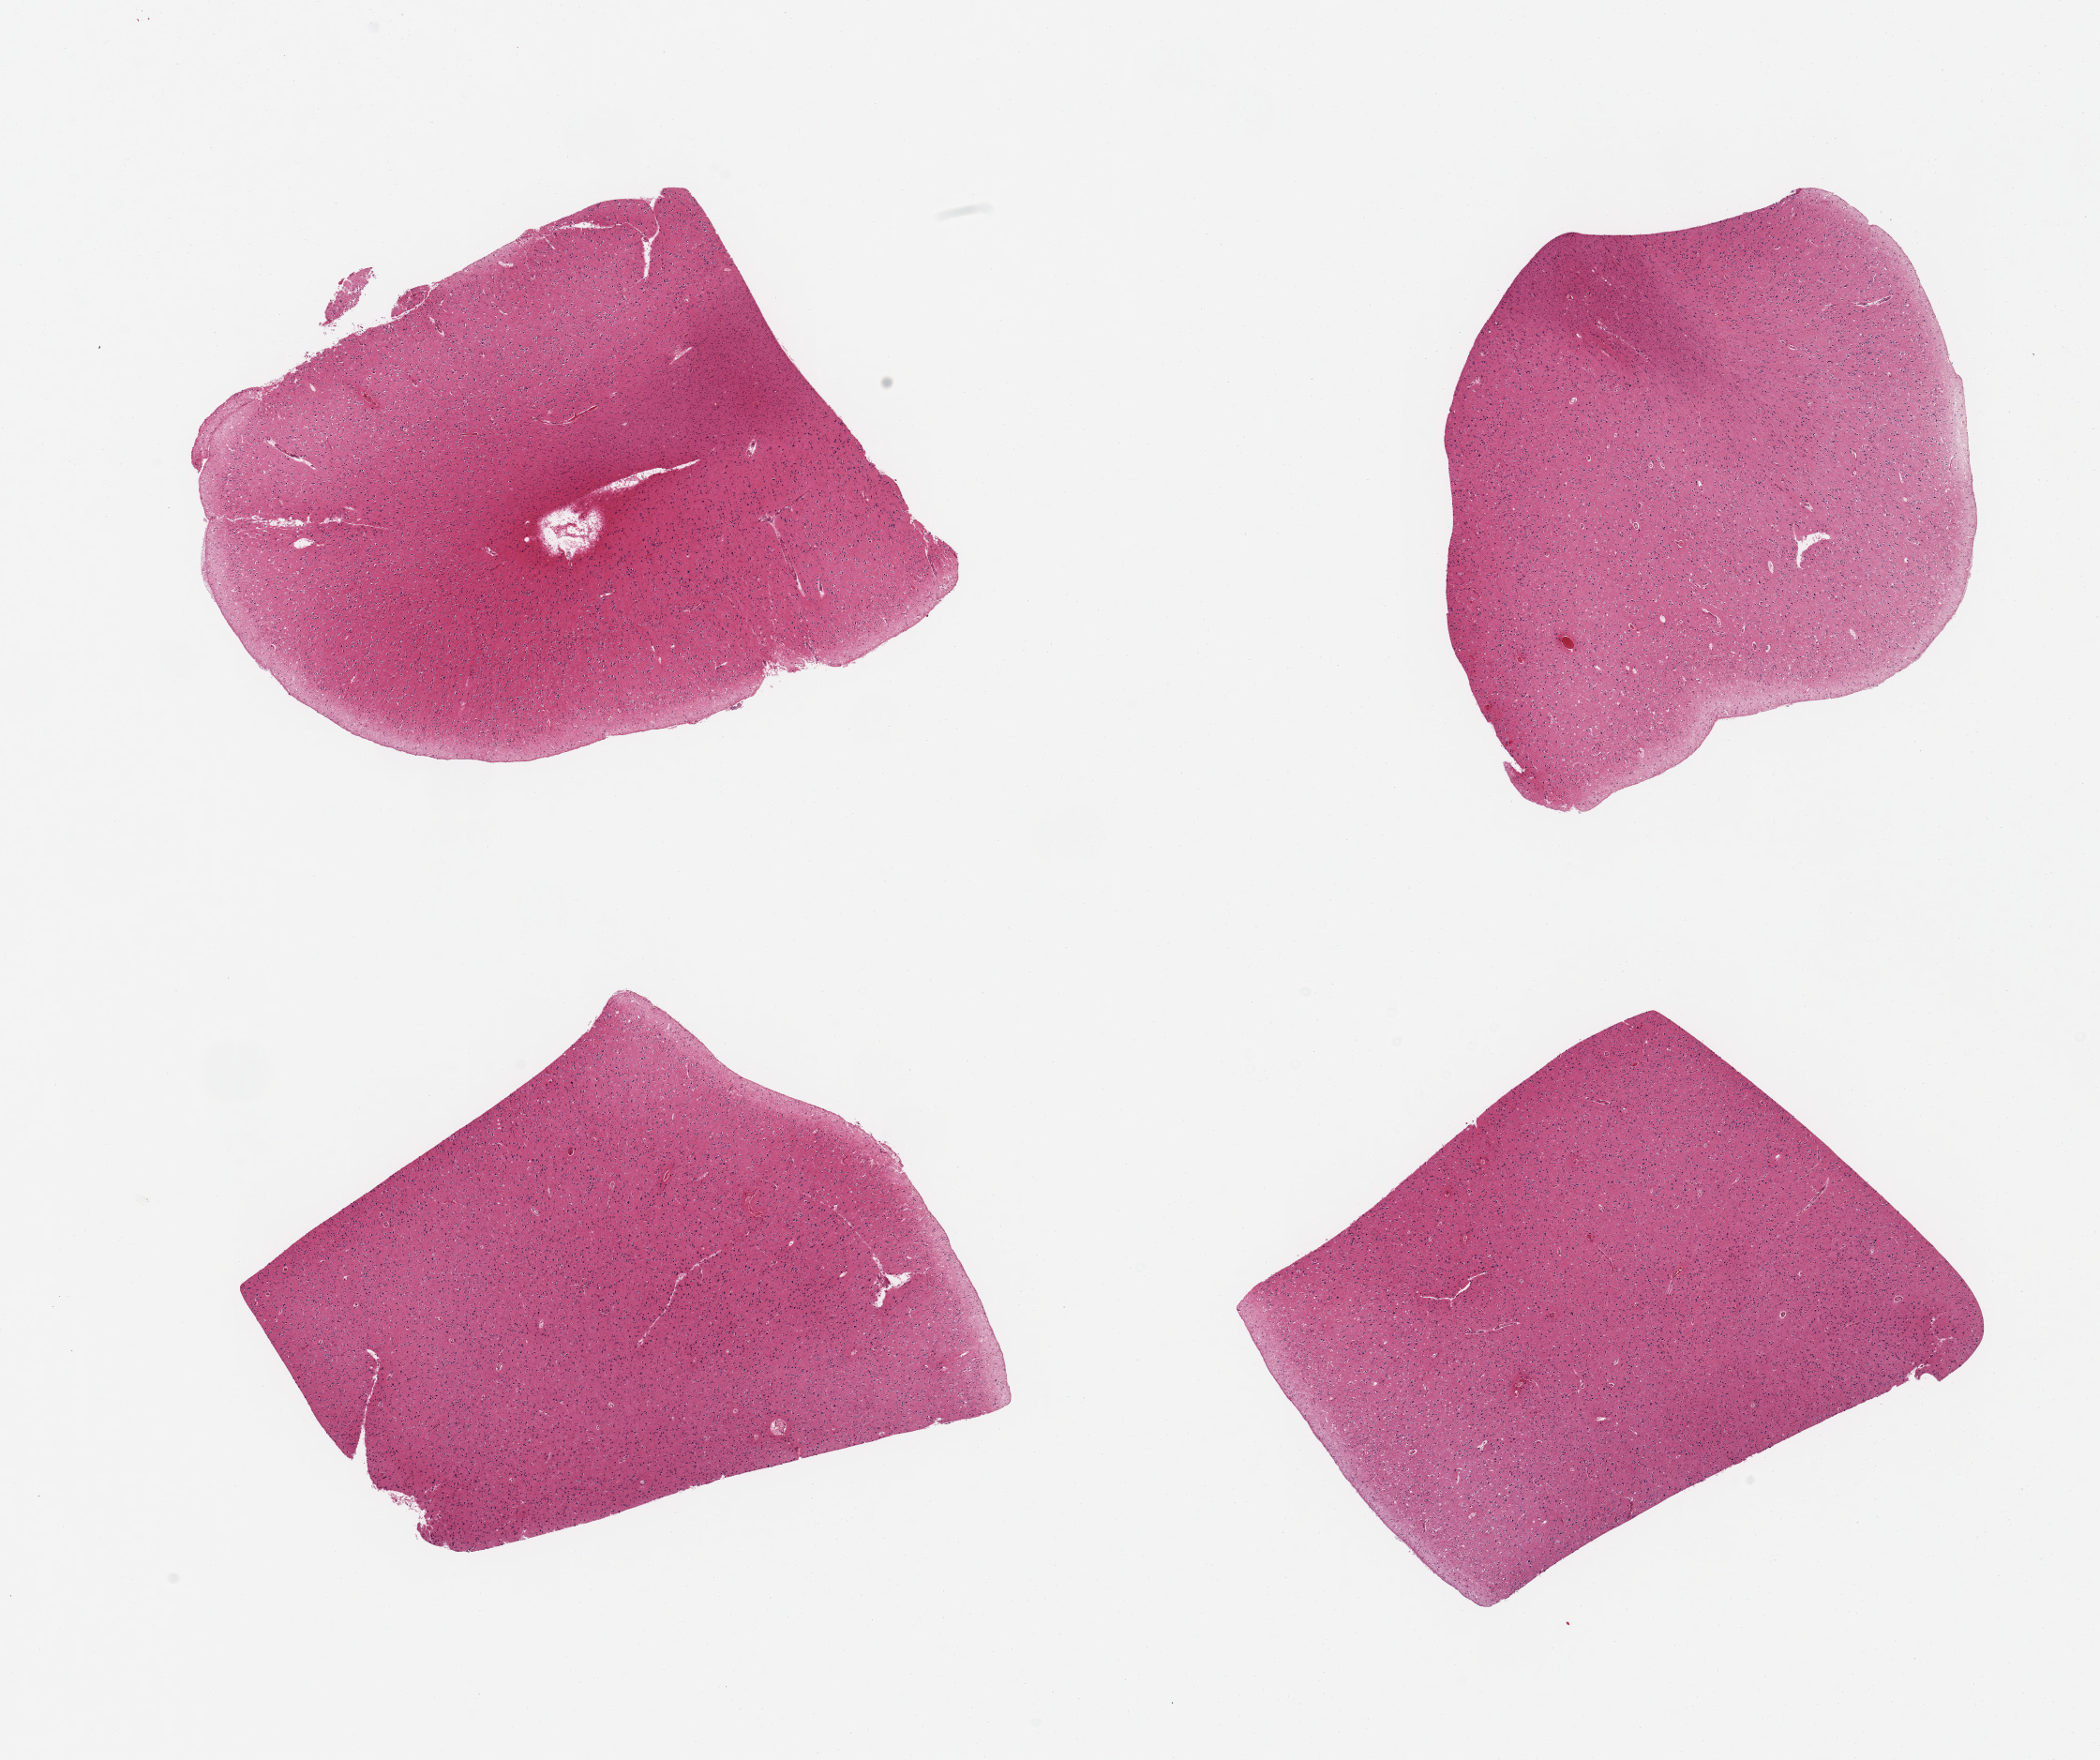
Hematoxylin and eosin (H&E) whole-slide image — shown as a low-resolution overview of the whole scanned area (about 17.7 x 14.8 mm). PAXgene-fixed paraffin-embedded (PFPE) section. Sampled site (target tissue): cerebral cortex. Tissue donor sample. Donor: male.
• pathologist's review note for this sample: 4 pieces